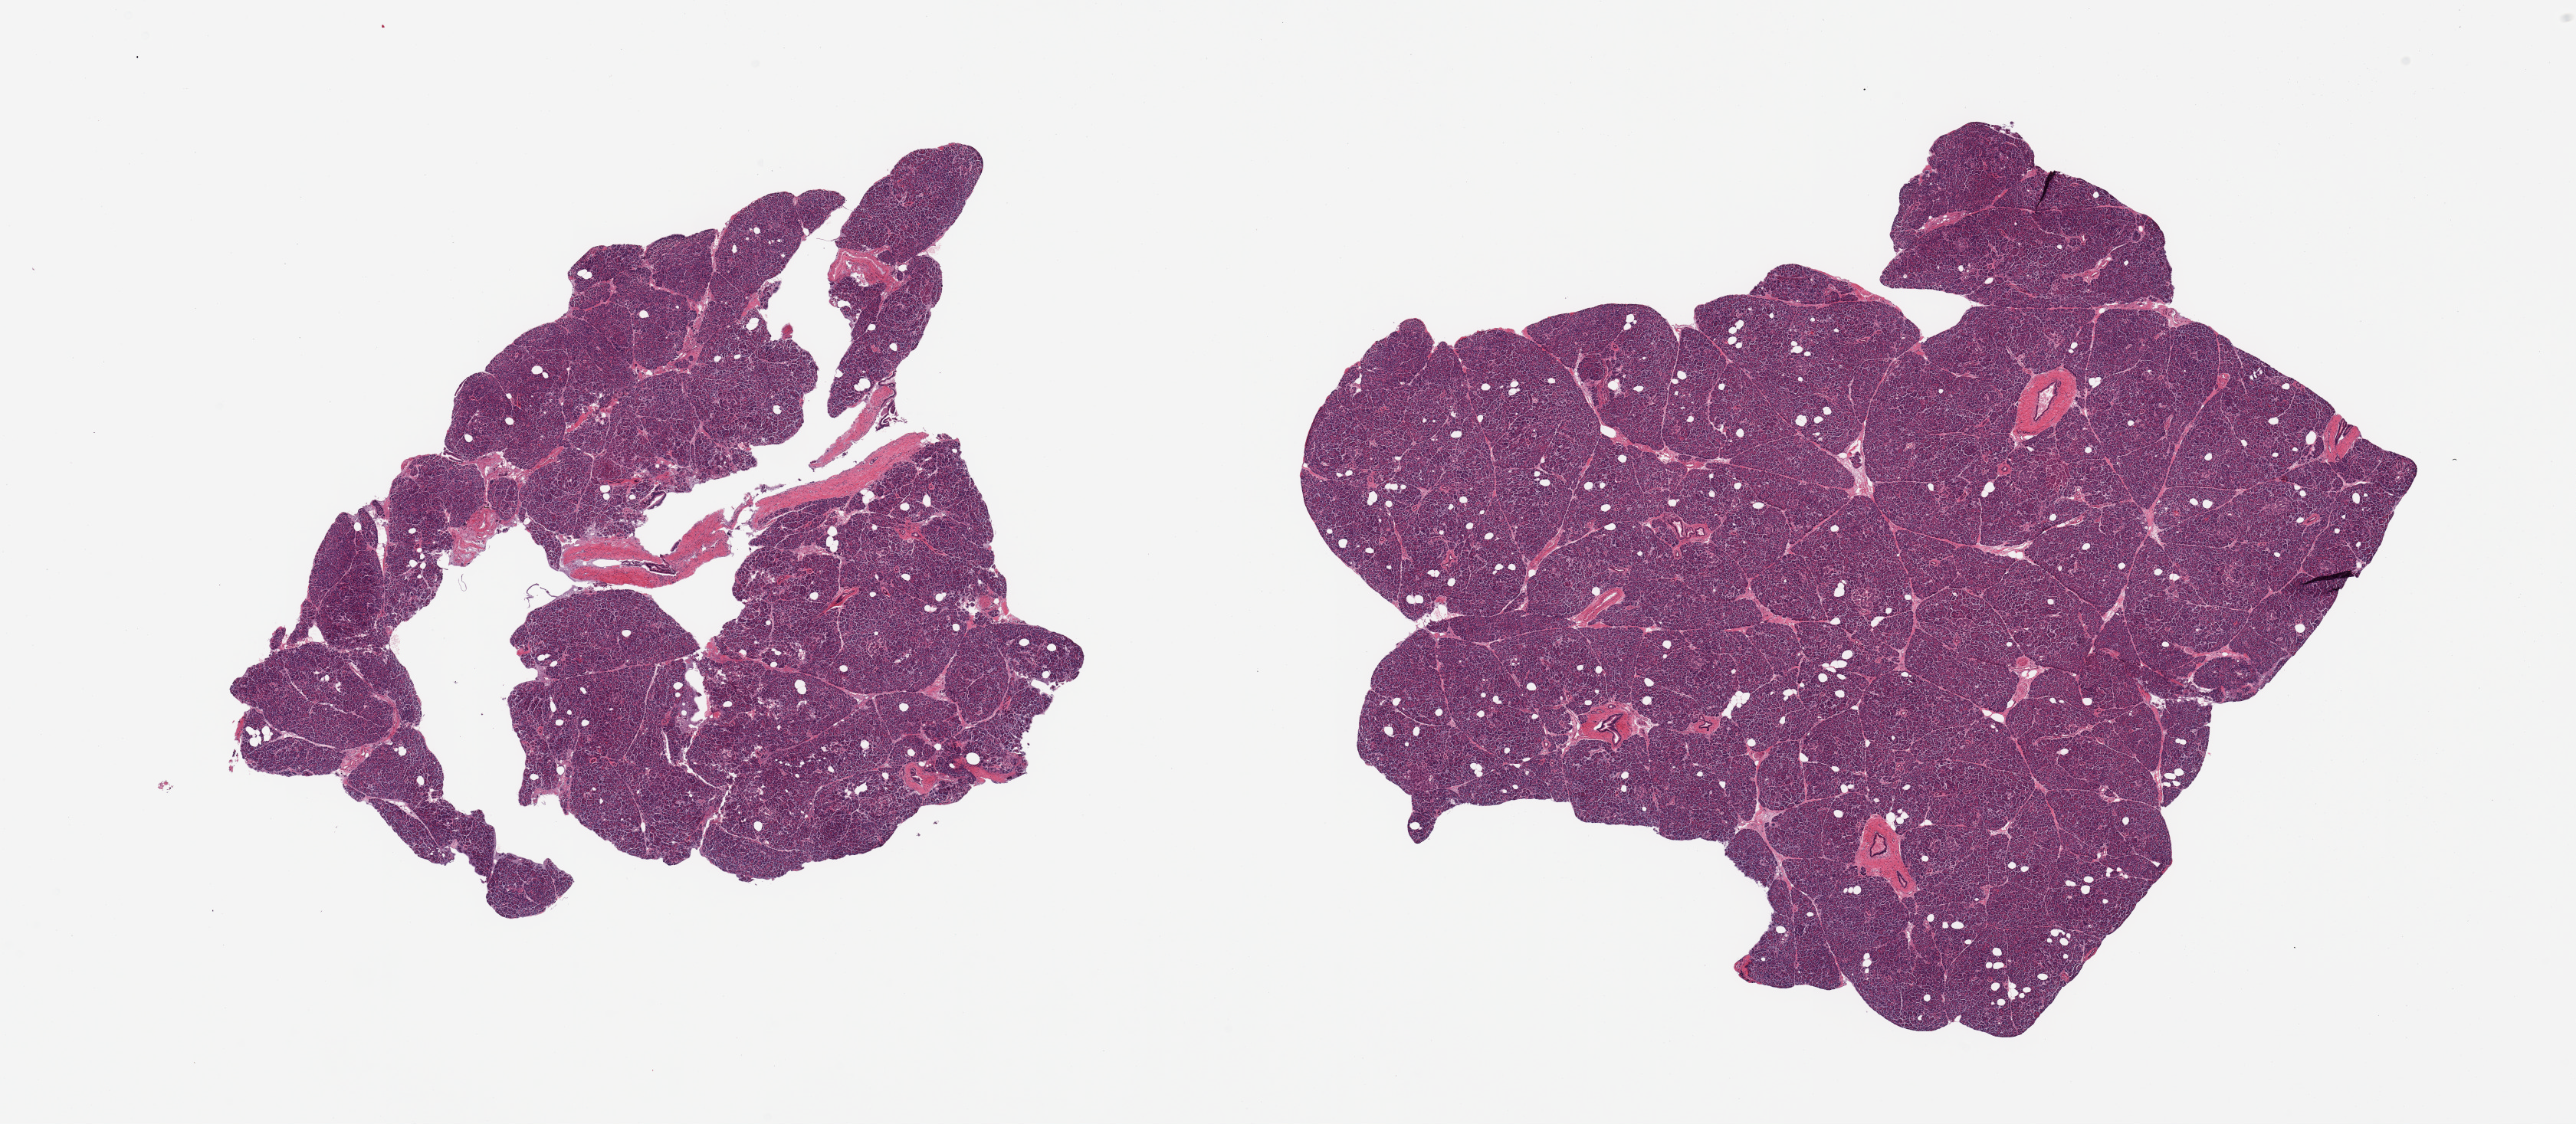
Digitized H&E-stained section, brightfield, whole scanned area (about 26.6 x 11.6 mm) shown as a low-resolution overview; PAXgene-fixed, paraffin-embedded tissue; section of pancreas (target tissue); donor tissue sample. Donor: female.
• review note (as recorded): 2 pieces; well preserved parenchyma and islets